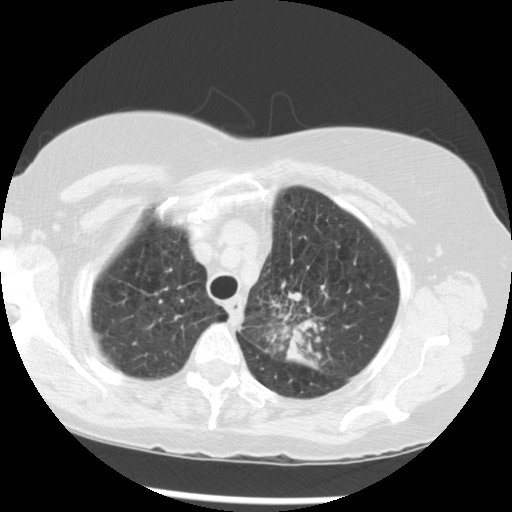
Low-dose screening chest CT, one axial slice; position 230 of 283 along the scan axis; reconstruction kernel STANDARD; lung window (W 1500 / L -600 HU); 2.5 mm slice thickness; 512 × 512 image matrix, field of view 330 × 330 mm.
Annotated regions visible in this slice (expert manual segmentation):
- lesion 1 (tumor, upper lobe of left lung): bounding box (x1, y1, x2, y2) in pixels: (285, 291, 320, 369)